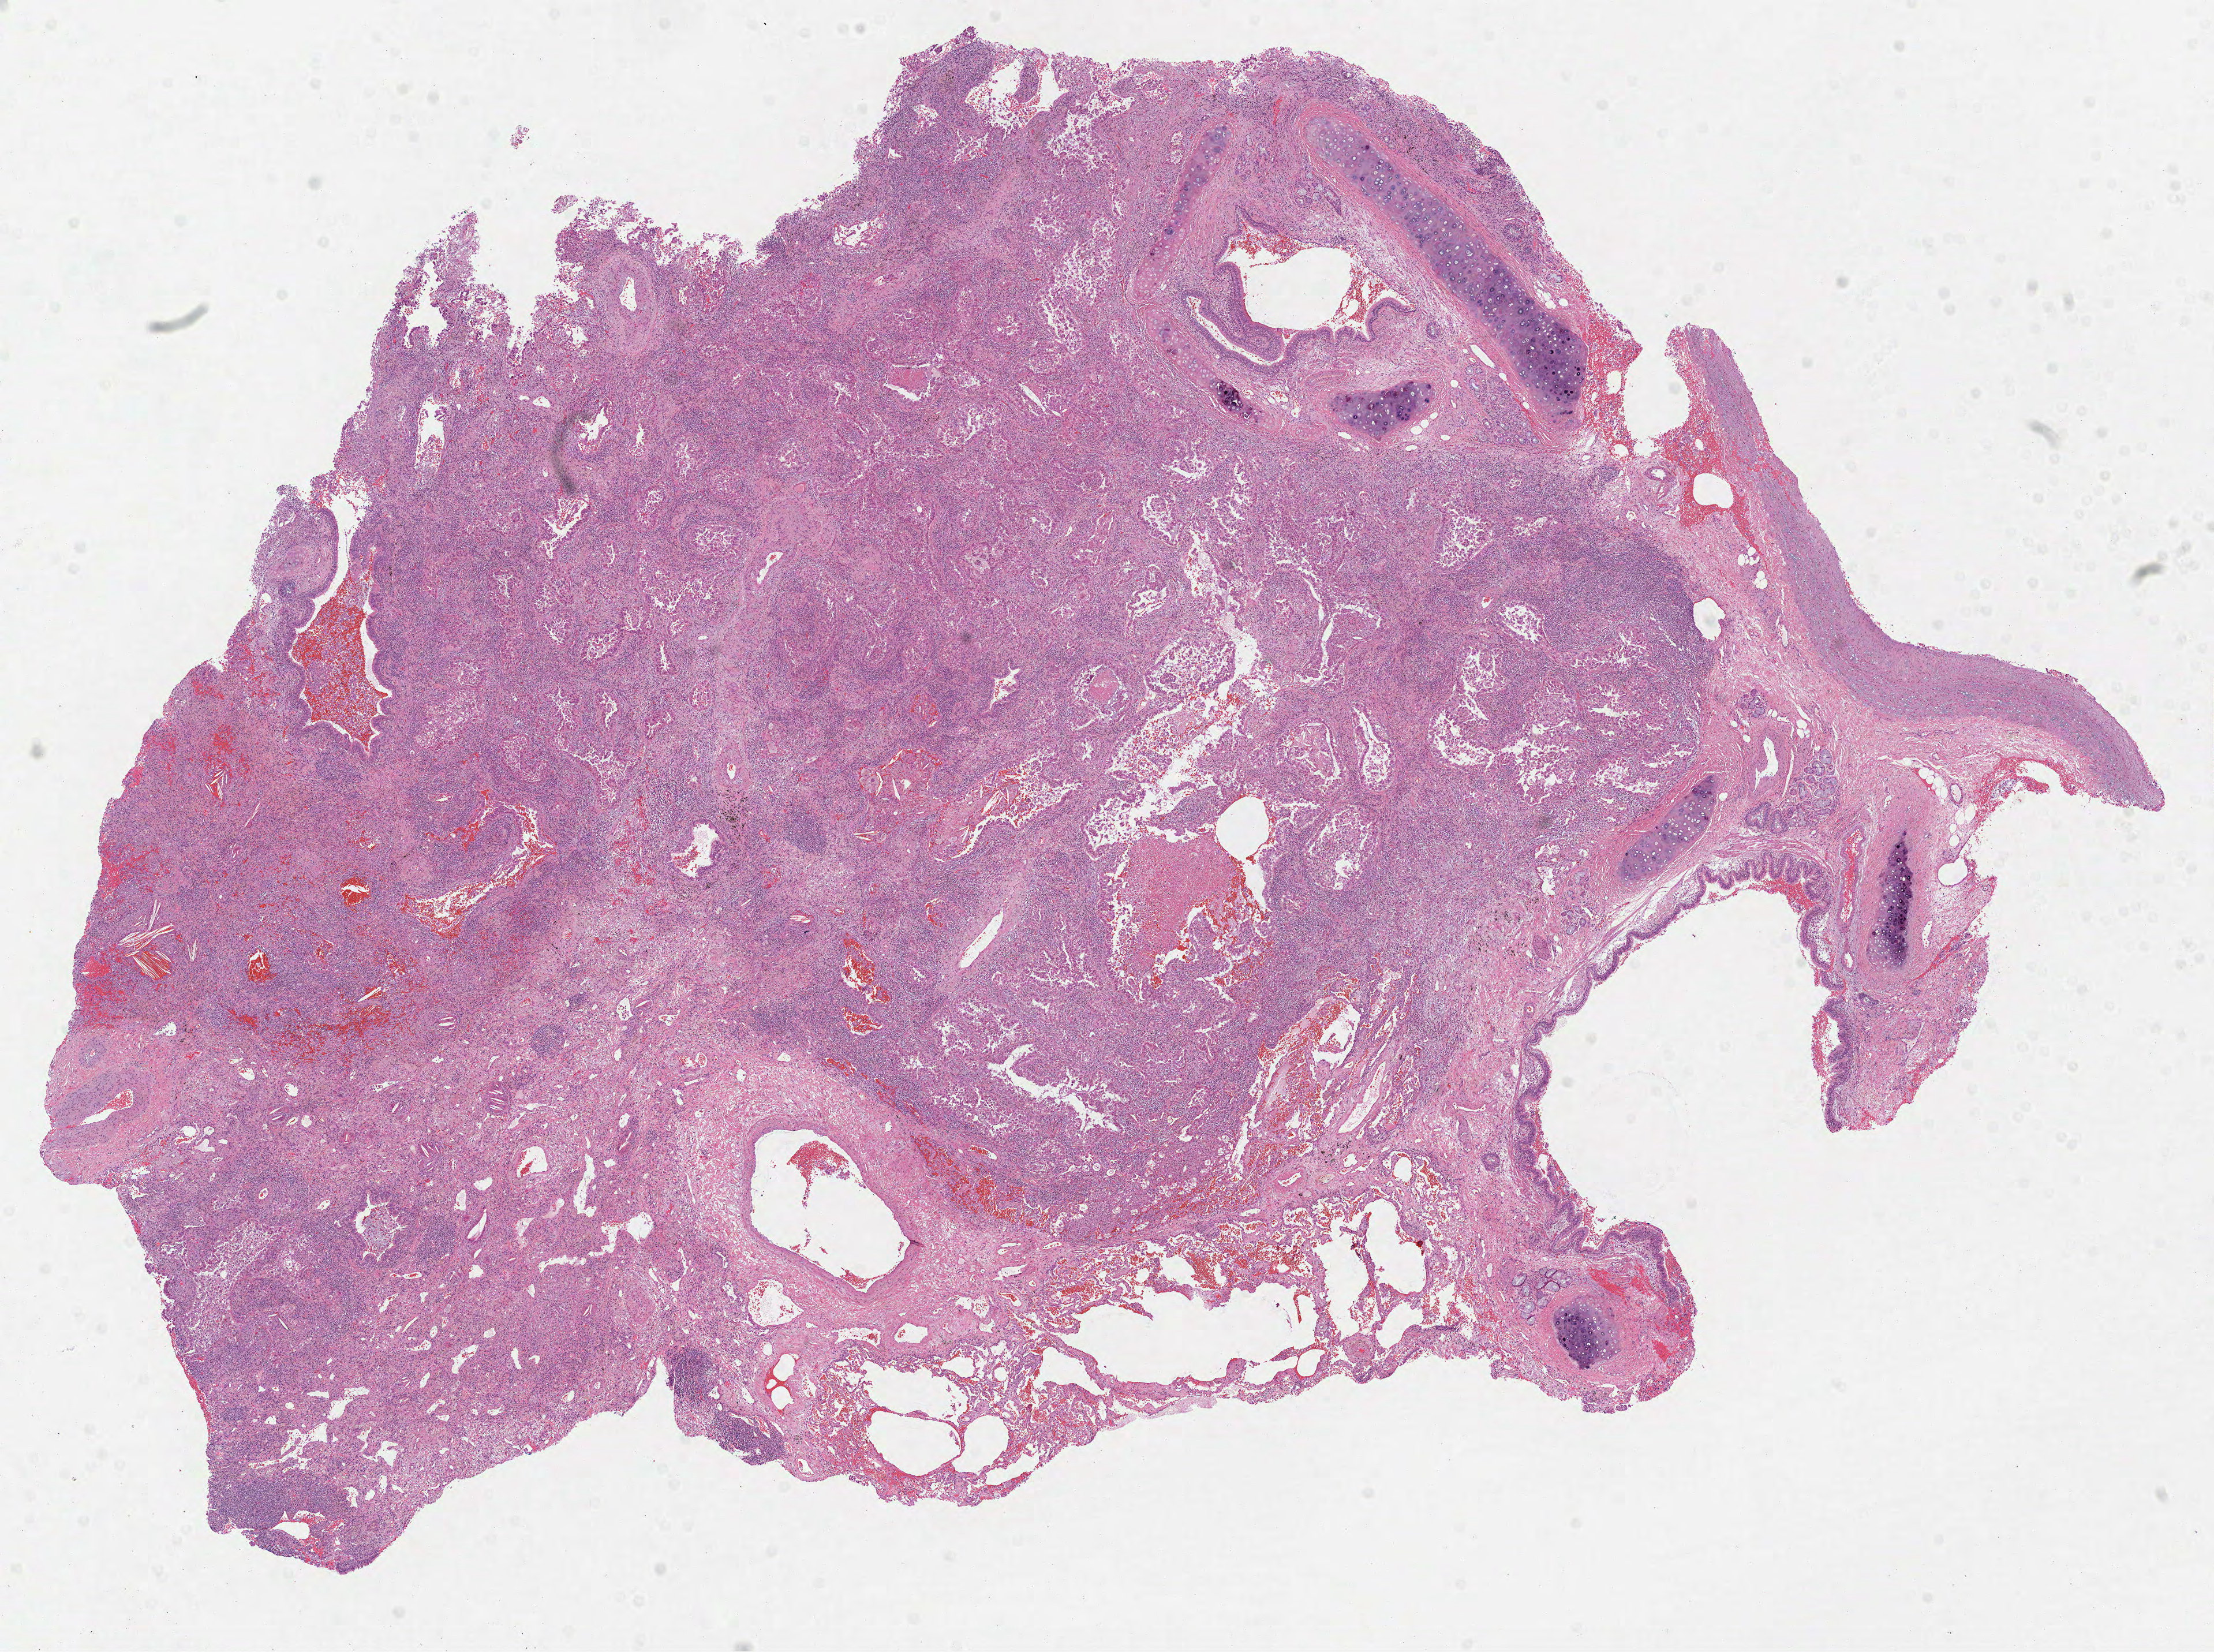
Whole-slide histology image, Hematoxylin and eosin (H&E) stained, whole scanned area (about 15.5 x 11.5 mm, from a 40x scan) shown as a low-resolution overview; FFPE section; lung, primary tumour sample. Male patient; age at initial diagnosis 77 years.
Laterality: left. AJCC pathologic stage: IIA (7th edition). Histologic diagnosis: Adenocarcinoma, NOS (upper lobe, lung).